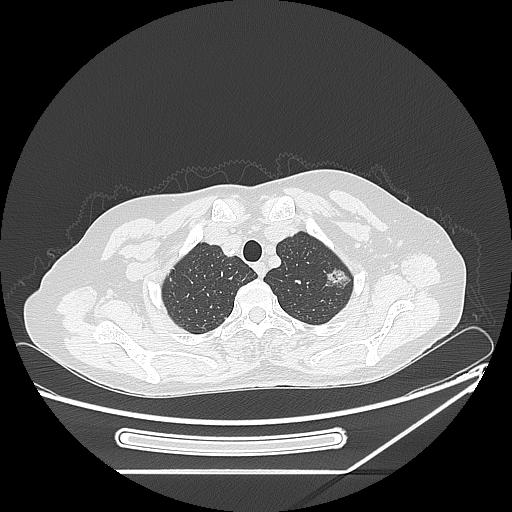
Chest CT, one axial slice. Slice 209 of 250 in the series (ordered by position). Reconstruction kernel LUNG. 120 kVp. Lung window (W 1500 / L -600 HU). 1.25 mm slice thickness. 512 × 512 image matrix, field of view 409 × 409 mm. Patient: female, 57 years. From the clinical record (not read from this slice): clinical TNM (as recorded): T1c N0 M0; histopathological grade: G2-3.
Structures marked on this image (bounding box drawn by a radiologist):
- lung tumour (recorded histology: adenocarcinoma): bounding box [x1, y1, x2, y2] px = [319, 265, 359, 297]